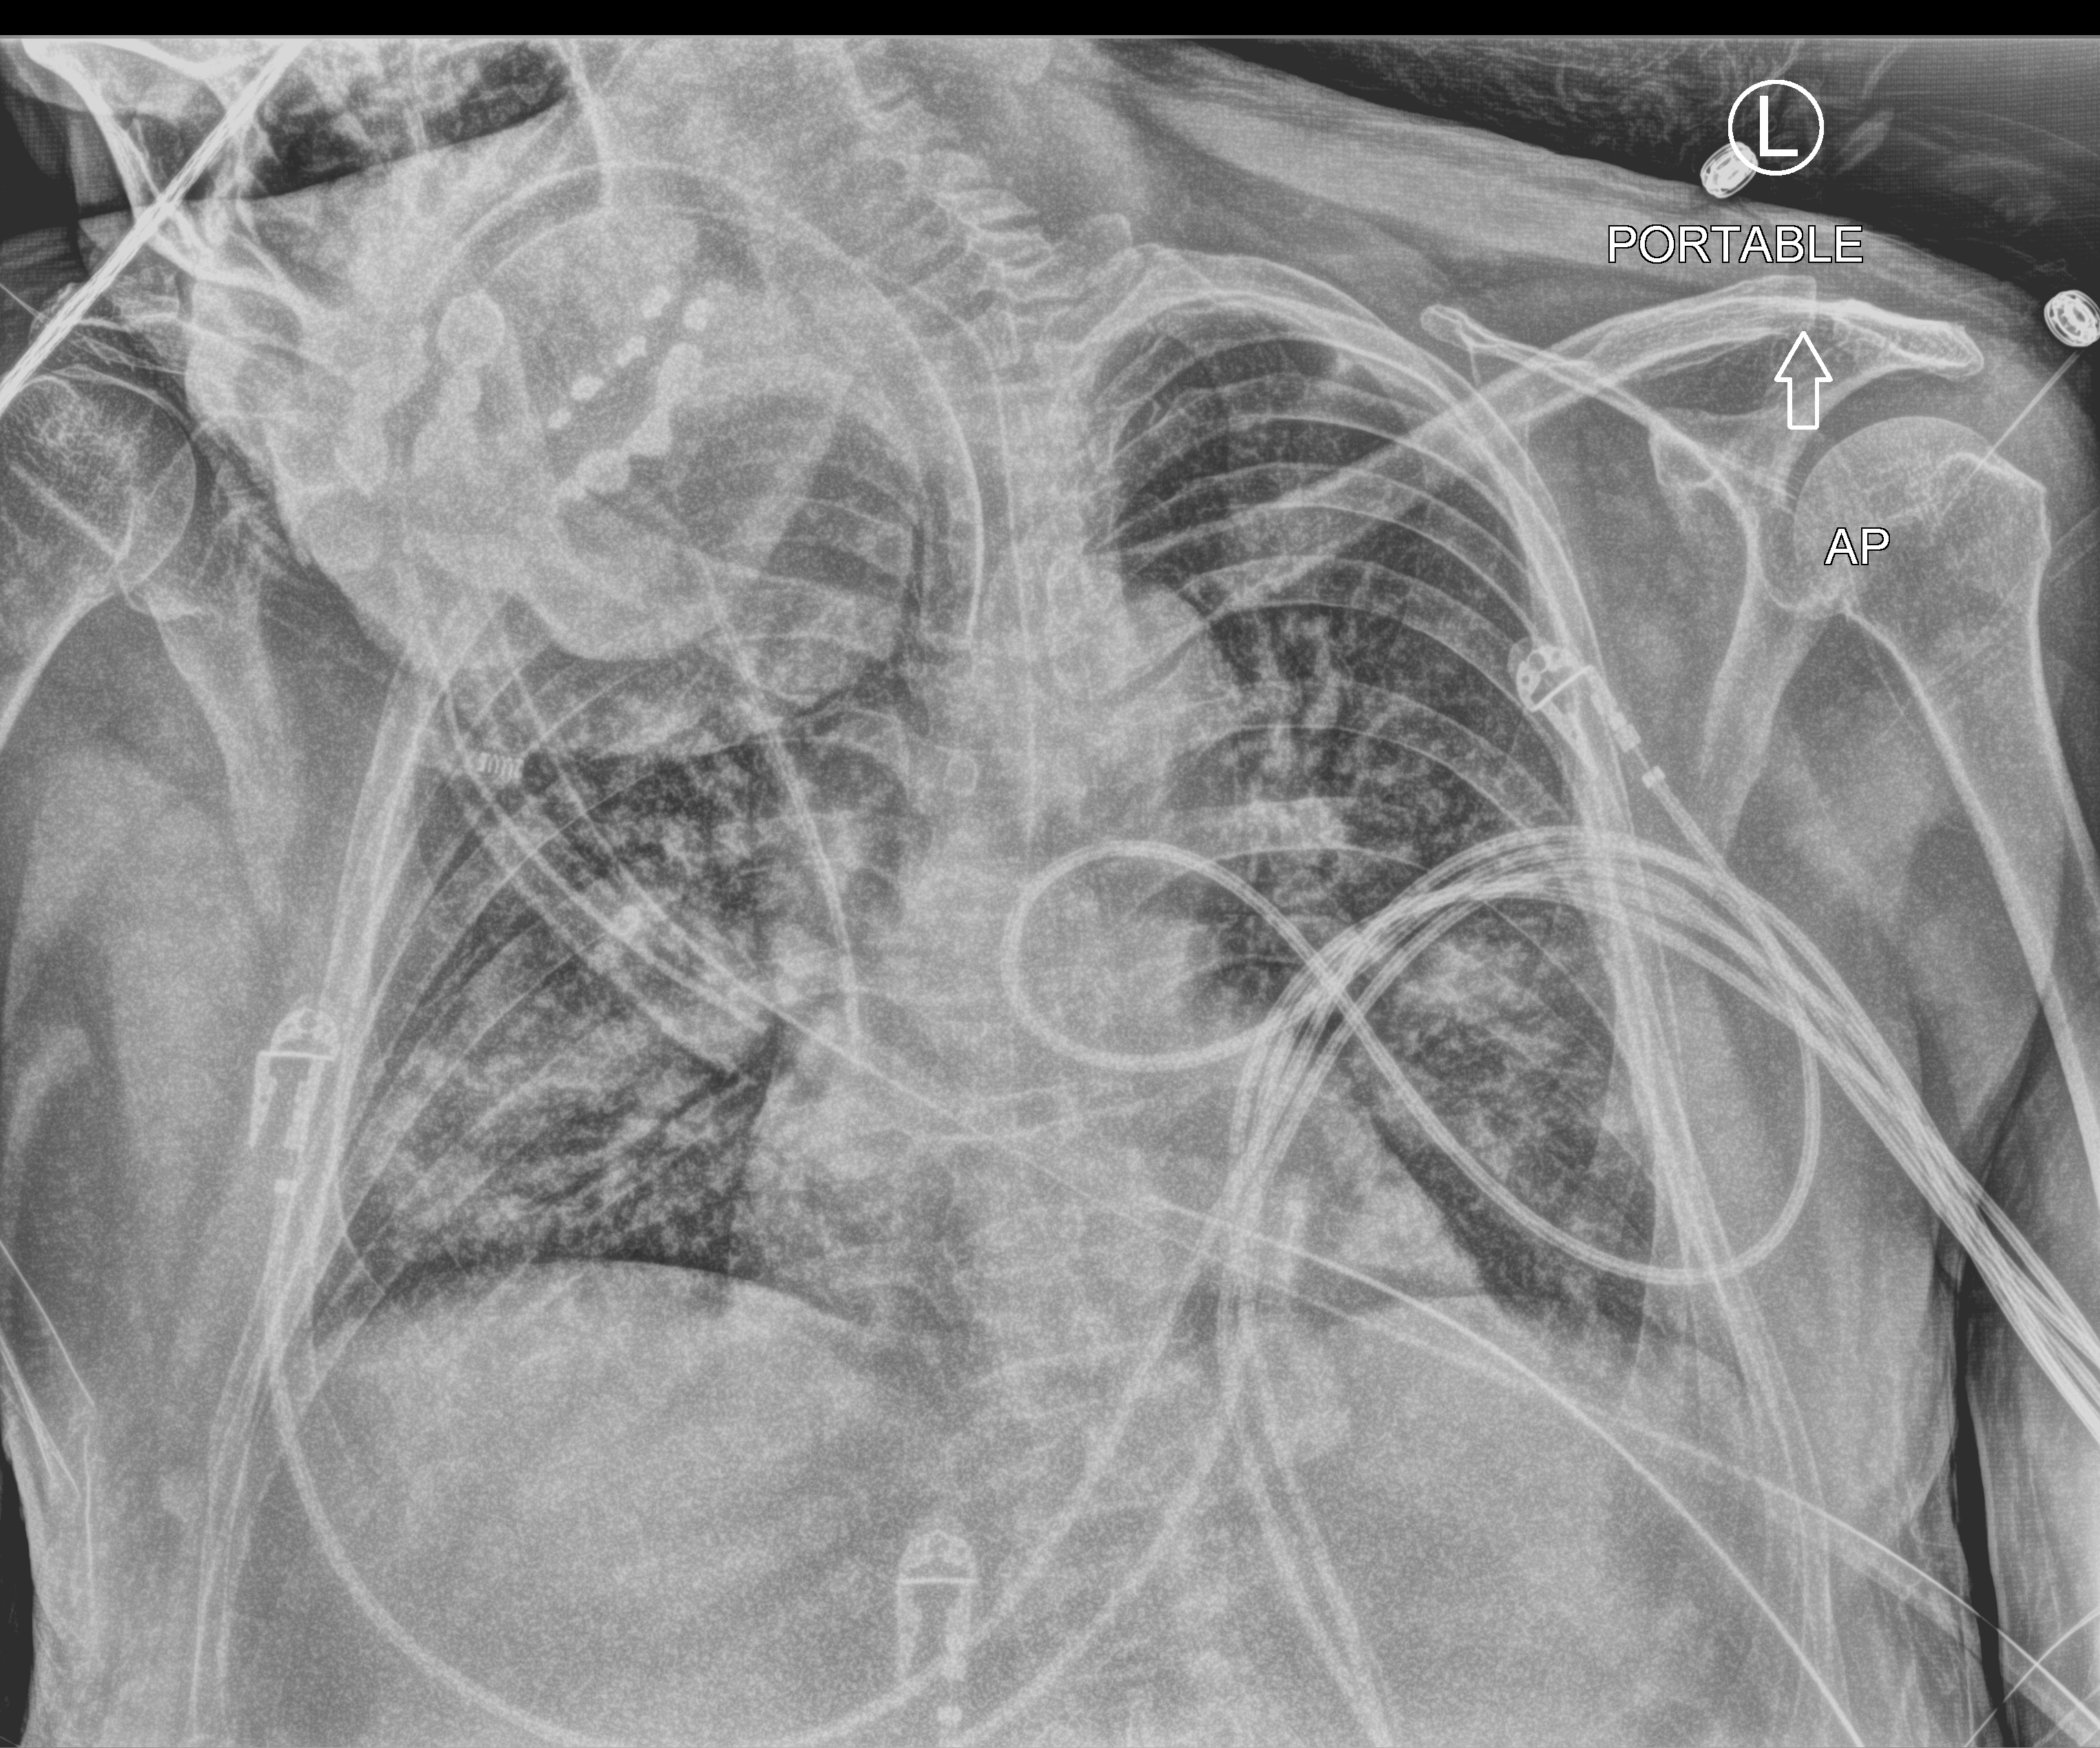
Bedside chest radiograph (computed radiography); anteroposterior (AP) projection. Patient hospitalised with COVID-19; male, aged 60–74 years.
Admission-level facts for this patient (not findings on this image; timing relative to this image not recorded): mechanically ventilated during this hospital stay: yes; other chronic lung disease (admission record): no.